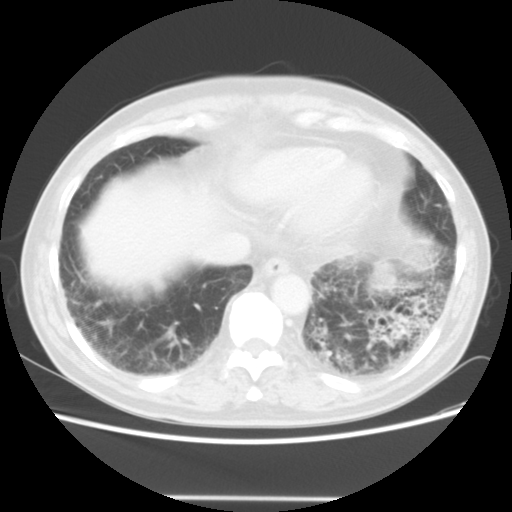
Chest CT, one axial slice; position 11 of 56 along the scan axis; 140 kVp; lung window (W 1500 / L -600 HU); 5 mm slice thickness; 512 × 512 image matrix, field of view 360 × 360 mm. Male patient, age 66 years. Case-level facts recorded for this patient, not image findings: clinical TNM (as recorded): T4 N3 M0; histopathological grade: G3.
Outlined on this slice (rectangle marked by the reading radiologist):
- lung tumour (recorded histology: small cell carcinoma): bounding box <366,259,404,297> (left, top, right, bottom; pixels)